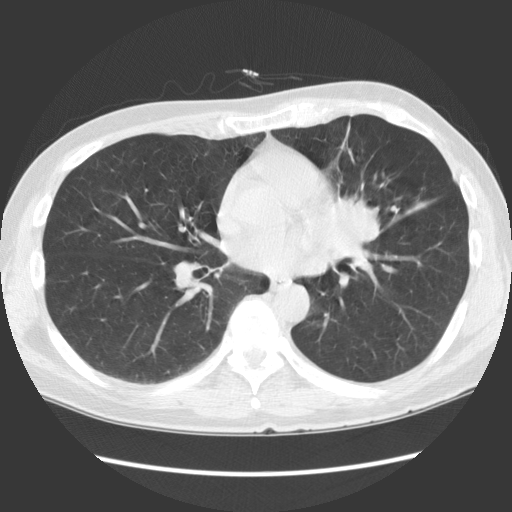
Chest CT (low-dose screening protocol), one axial image. First (baseline) screen. Lung window (W 1500 / L -600 HU). 2.5 mm slice thickness. 512 × 512 image matrix, field of view 360 × 360 mm. Male, age 61 years at enrolment.
Expert reader's lesion annotation, bounding box [x1, y1, x2, y2] px = [306, 182, 401, 282]. Reader record for this screening exam (exam-level; its link to the box is not recorded): non-calcified nodule or mass ≥4 mm, lingula, 35 × 35 mm, spiculated (stellate) margins, soft tissue attenuation. Official screen result: positive, change unspecified: nodule(s) >= 4 mm or enlarging nodule(s), mass(es), or other non-specific abnormalities suspicious for lung cancer. Later outcome: lung cancer diagnosed 58 days after this screen — squamous cell carcinoma, NOS, left hilum, left main stem bronchus, poorly differentiated (G3), stage IA (AJCC 6th edition), 40 mm at pathology.